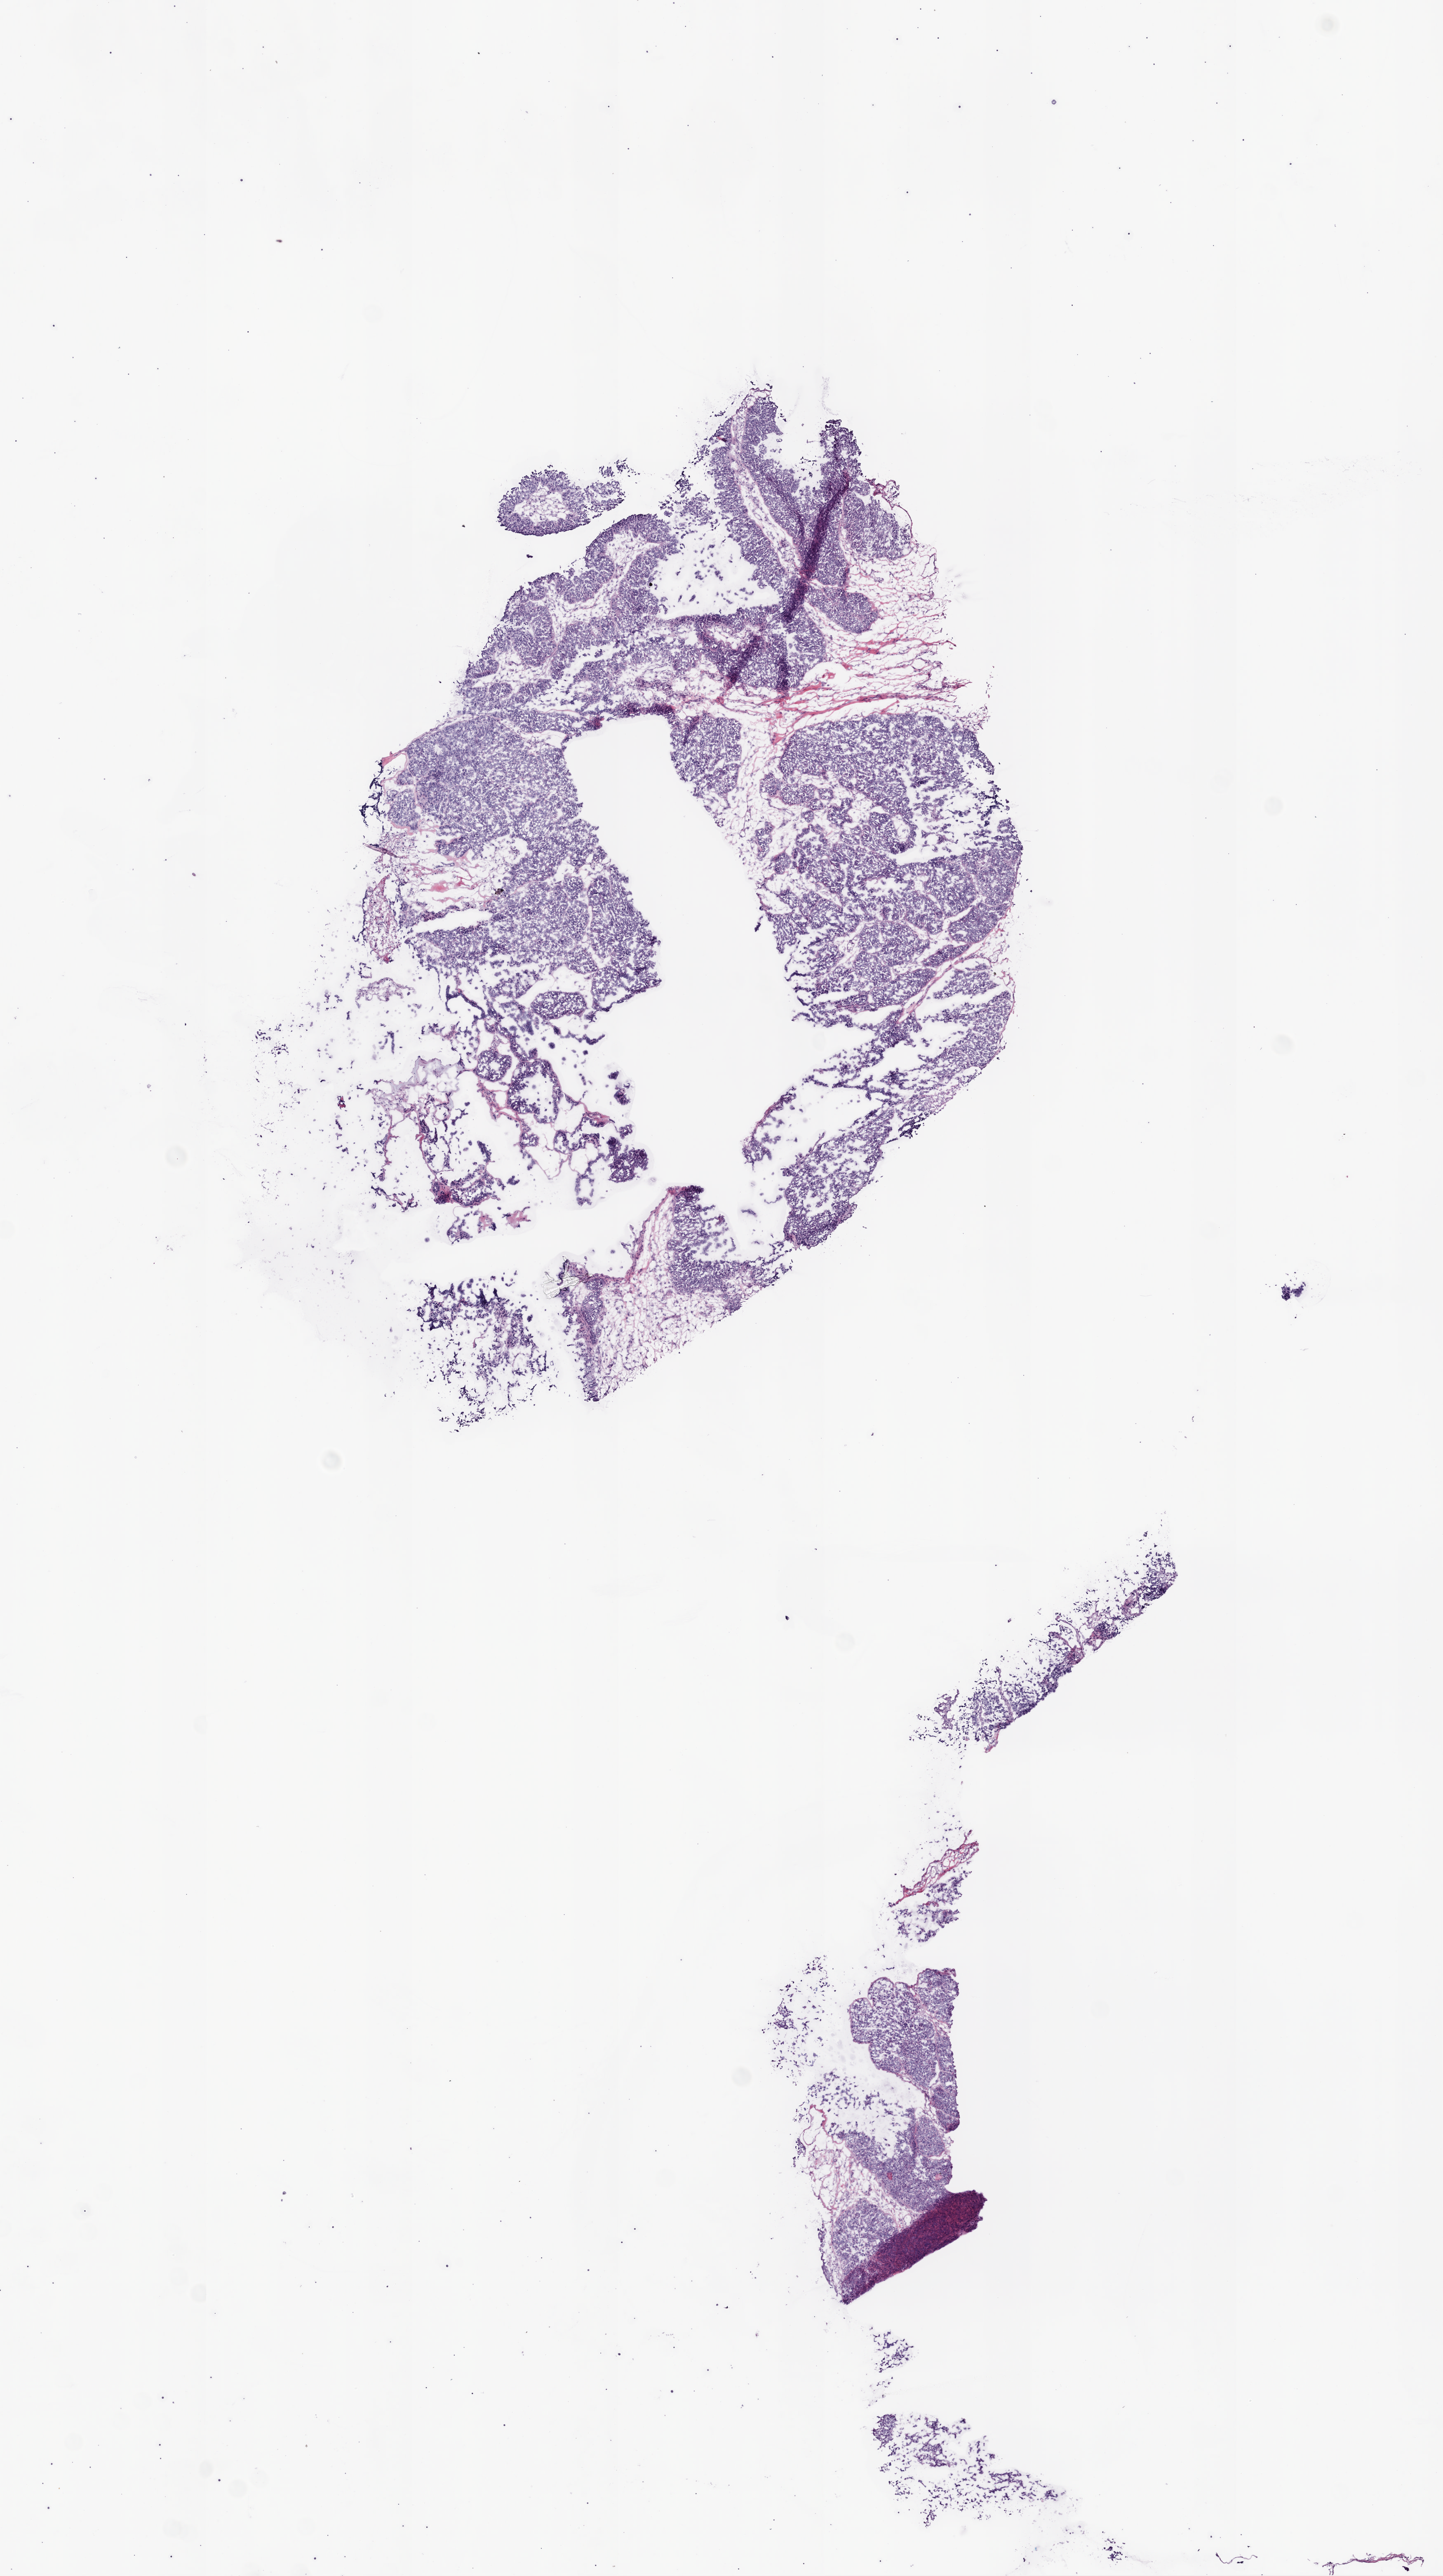
Digitized Hematoxylin and eosin (H&E) stained tissue section (whole slide), low-resolution overview of the scanned area, about 7.0 x 12.5 mm. Frozen section from the bottom of the tissue portion. Primary tumour sample from the ovary. Patient: female, age at initial diagnosis 59 years. Histologic grade: G3 (poorly differentiated). Pathologist review of this section (percent, as recorded): tumour cells 90%, tumour nuclei 90%, normal cells 0%, stromal cells 10%, necrosis 0%. Infiltration values recorded for this section: lymphocyte infiltration 0%, monocyte infiltration 0%, neutrophil infiltration 0%.
Laterality: bilateral. FIGO stage: IIIC. Pathologic diagnosis: Serous cystadenocarcinoma, NOS.